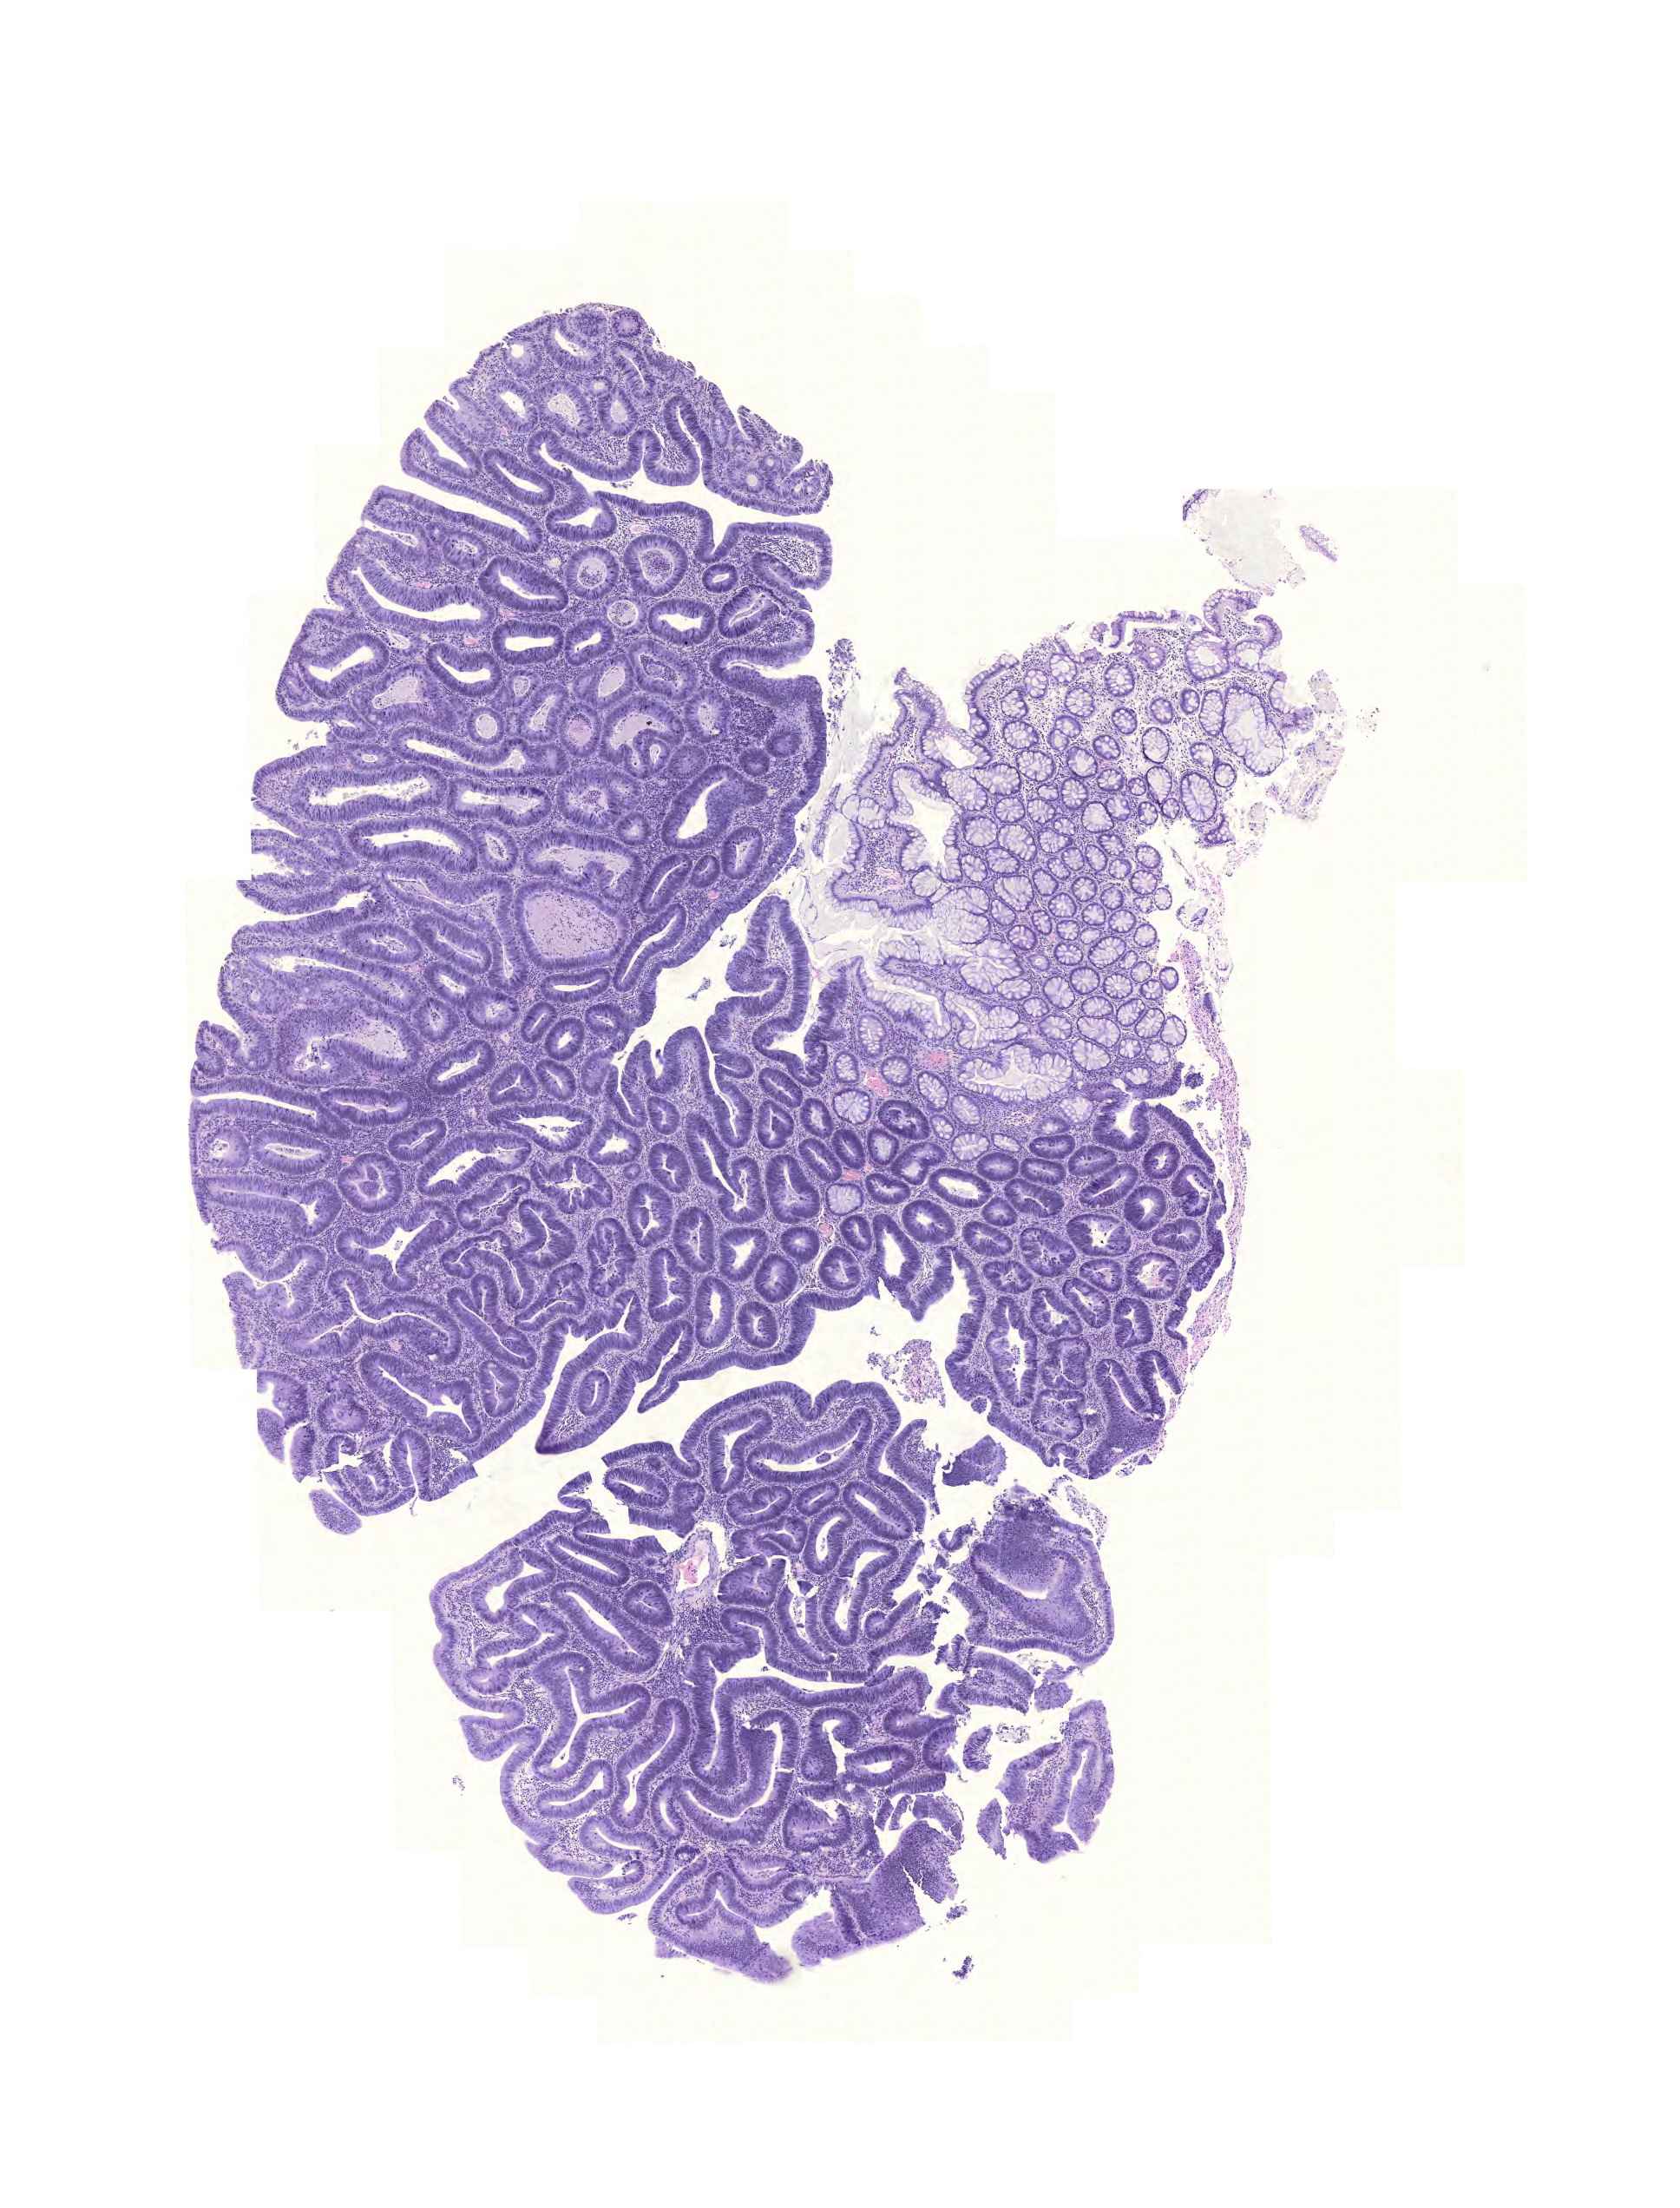
Hematoxylin and eosin (H&E) stained whole-slide image, shown as a low-resolution overview of the whole scanned area (about 7.2 x 9.5 mm, from a 20x scan); formalin-fixed paraffin-embedded (FFPE) diagnostic section; sample: primary tumour, rectum. Patient: female, age at initial diagnosis 66 years.
Pathologic diagnosis: Adenocarcinoma, NOS.